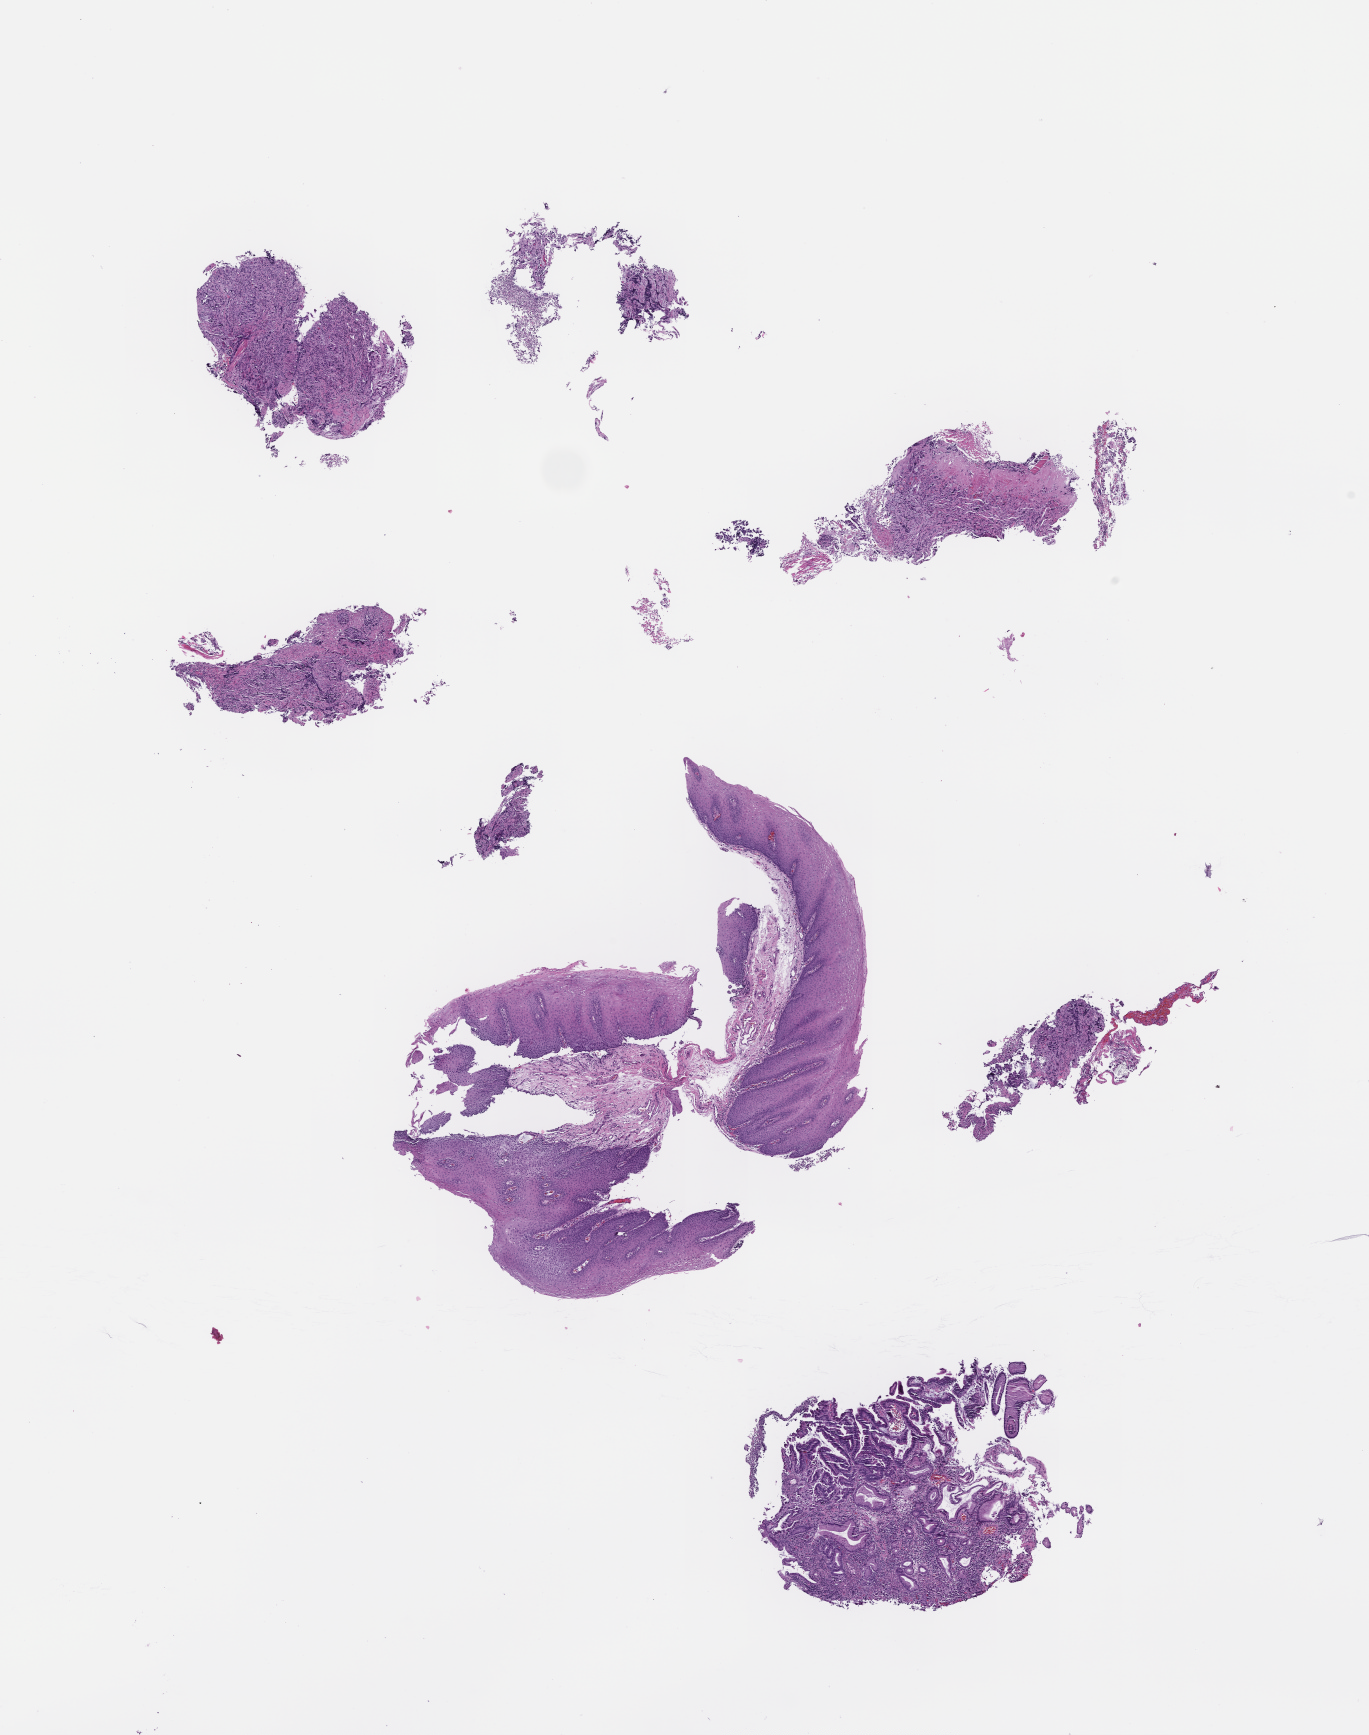
Digitized H&E-stained section, low-resolution overview of the scanned area, about 11.1 x 14.0 mm; formalin-fixed, paraffin-embedded (FFPE) tissue. Patient: male.
This section: metastatic tumor tissue. Primary diagnosis of the patient: Adenocarcinoma of the Gastroesophageal Junction.